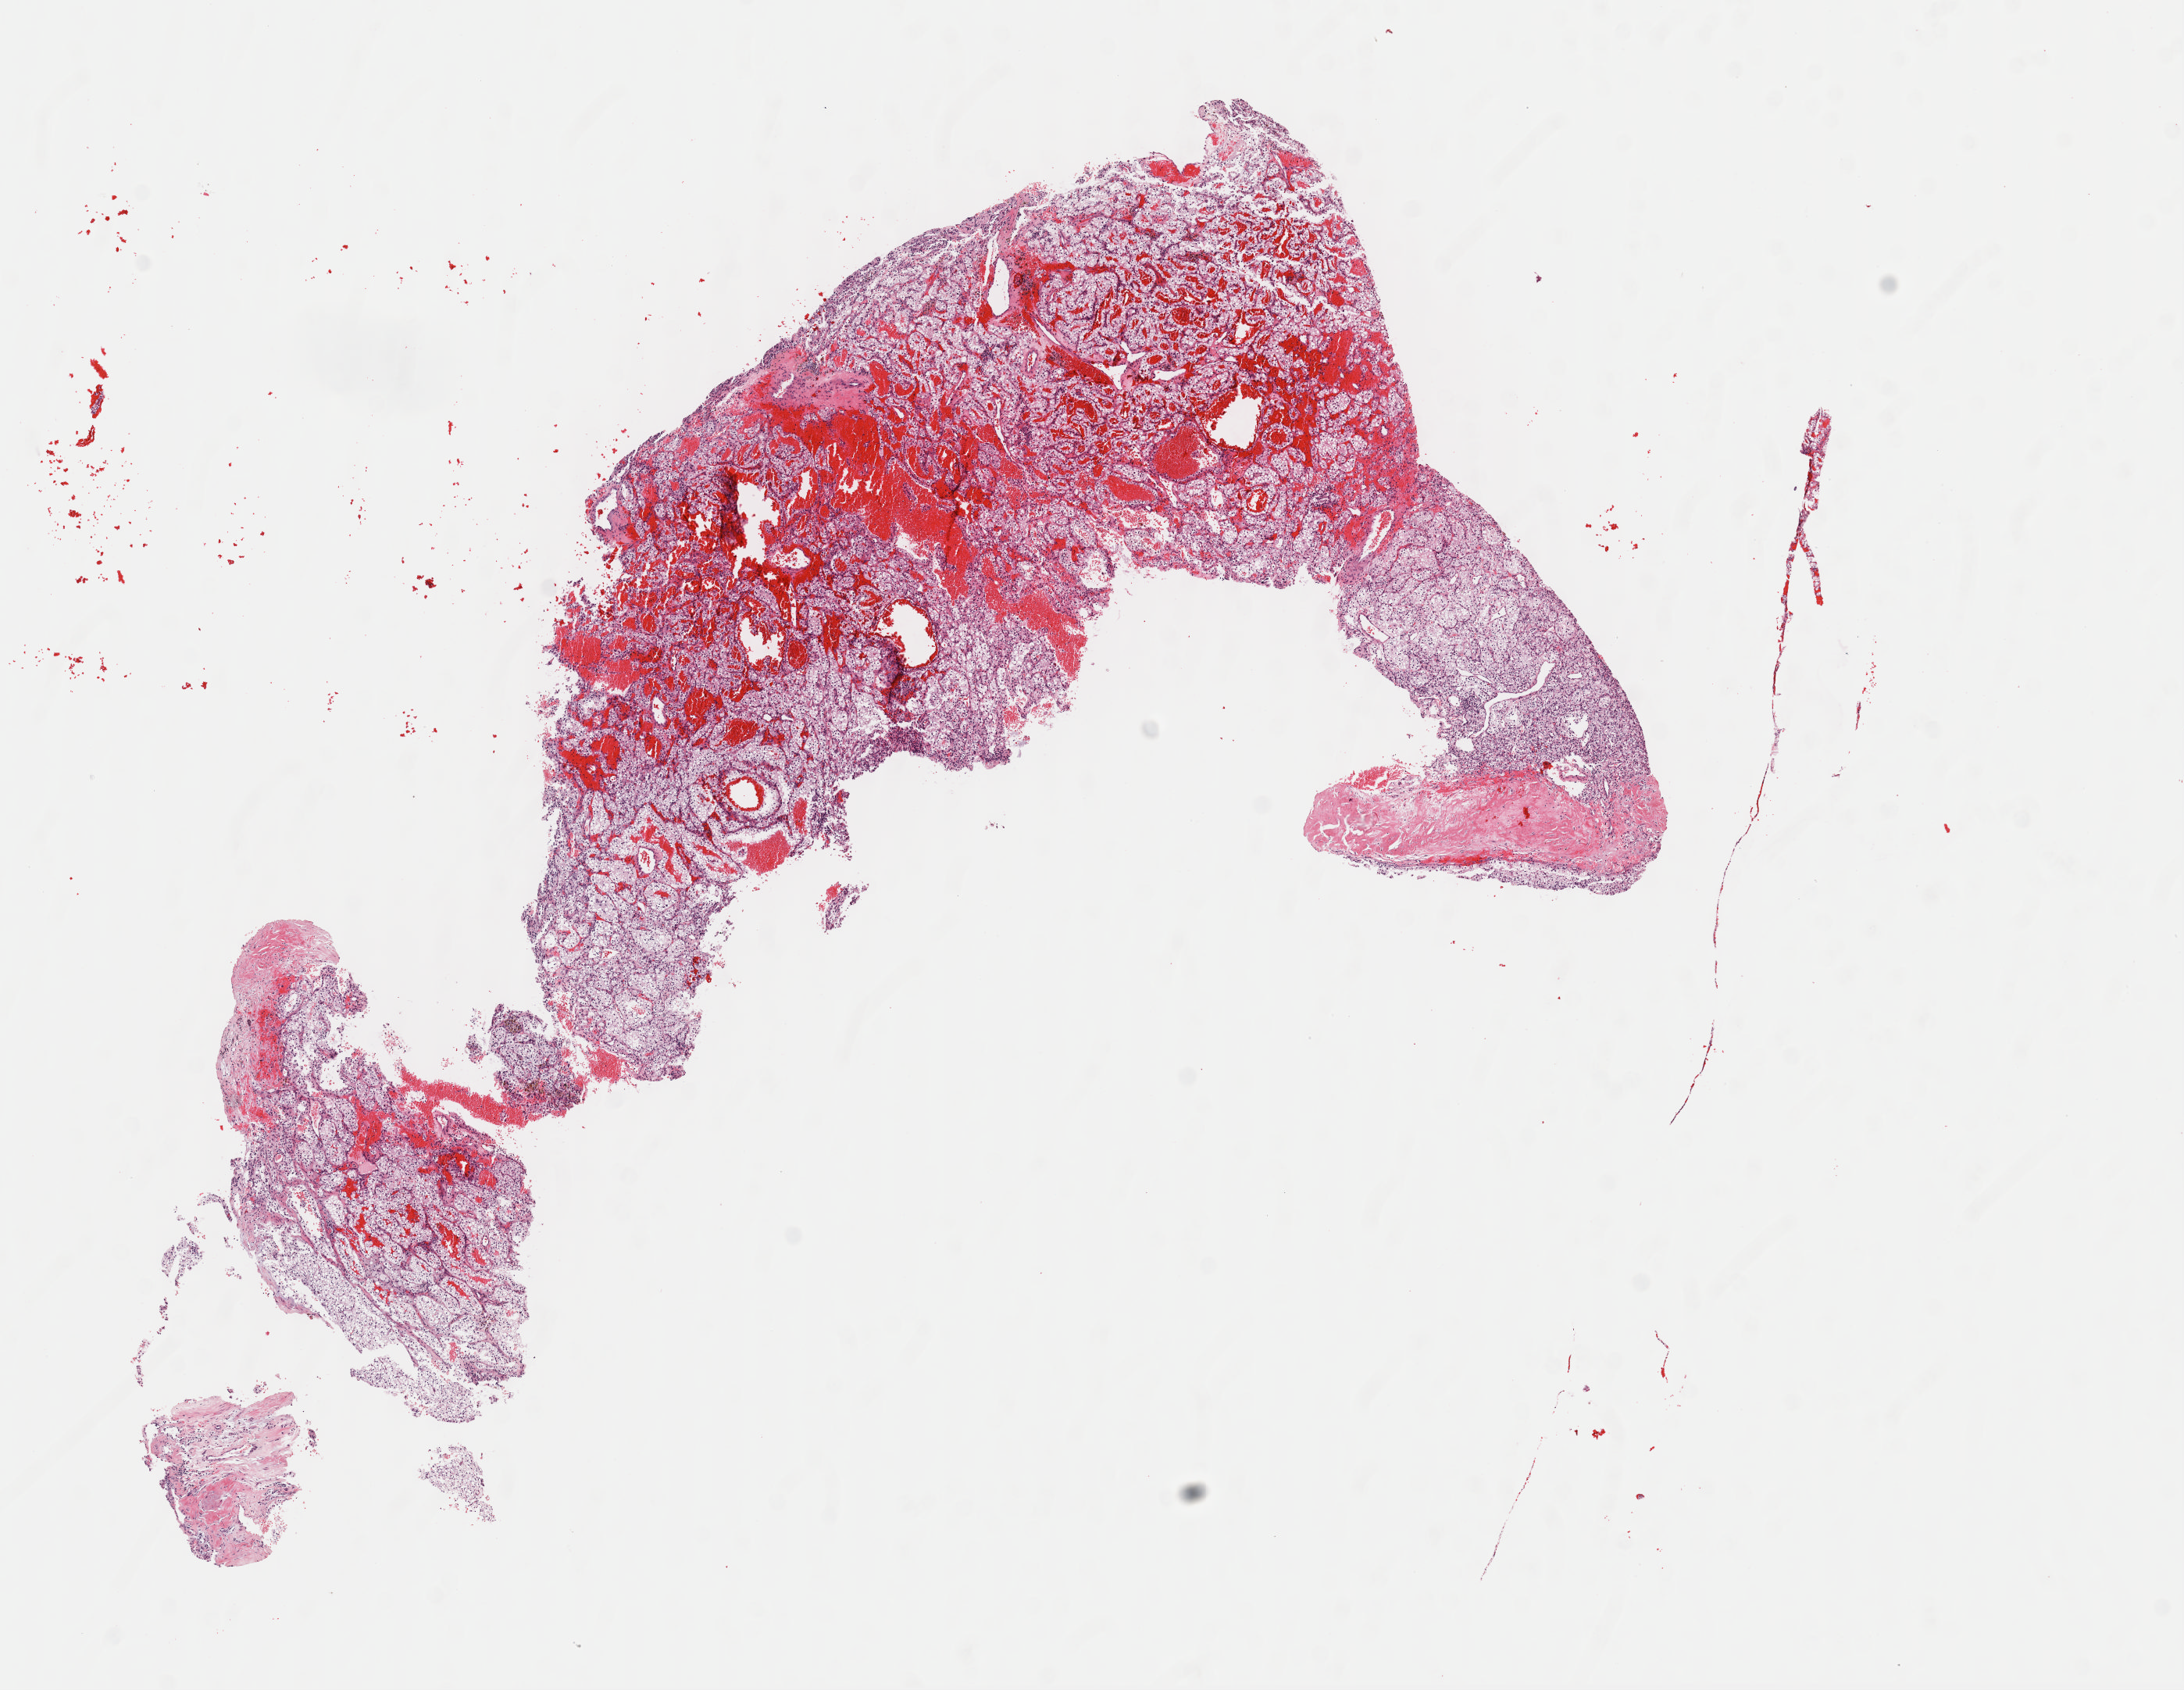
Hematoxylin and eosin (H&E) stained whole-slide image — whole scanned area (about 11.0 x 8.5 mm, slide scanned at 40x) shown as a low-resolution overview, frozen section, kidney, primary tumour sample. Male patient; age at initial diagnosis 56 years. Histologic grade: G2 (moderately differentiated). Slide review estimates, as recorded: tumour cells 85%, tumour nuclei 90%, normal cells 0%, stromal cells 15%, necrosis 0%. Inflammatory infiltration, as recorded: lymphocyte infiltration 3%, monocyte infiltration 1%, neutrophil infiltration 1%.
* diagnosis: Clear cell adenocarcinoma, NOS
* AJCC pathologic stage: I